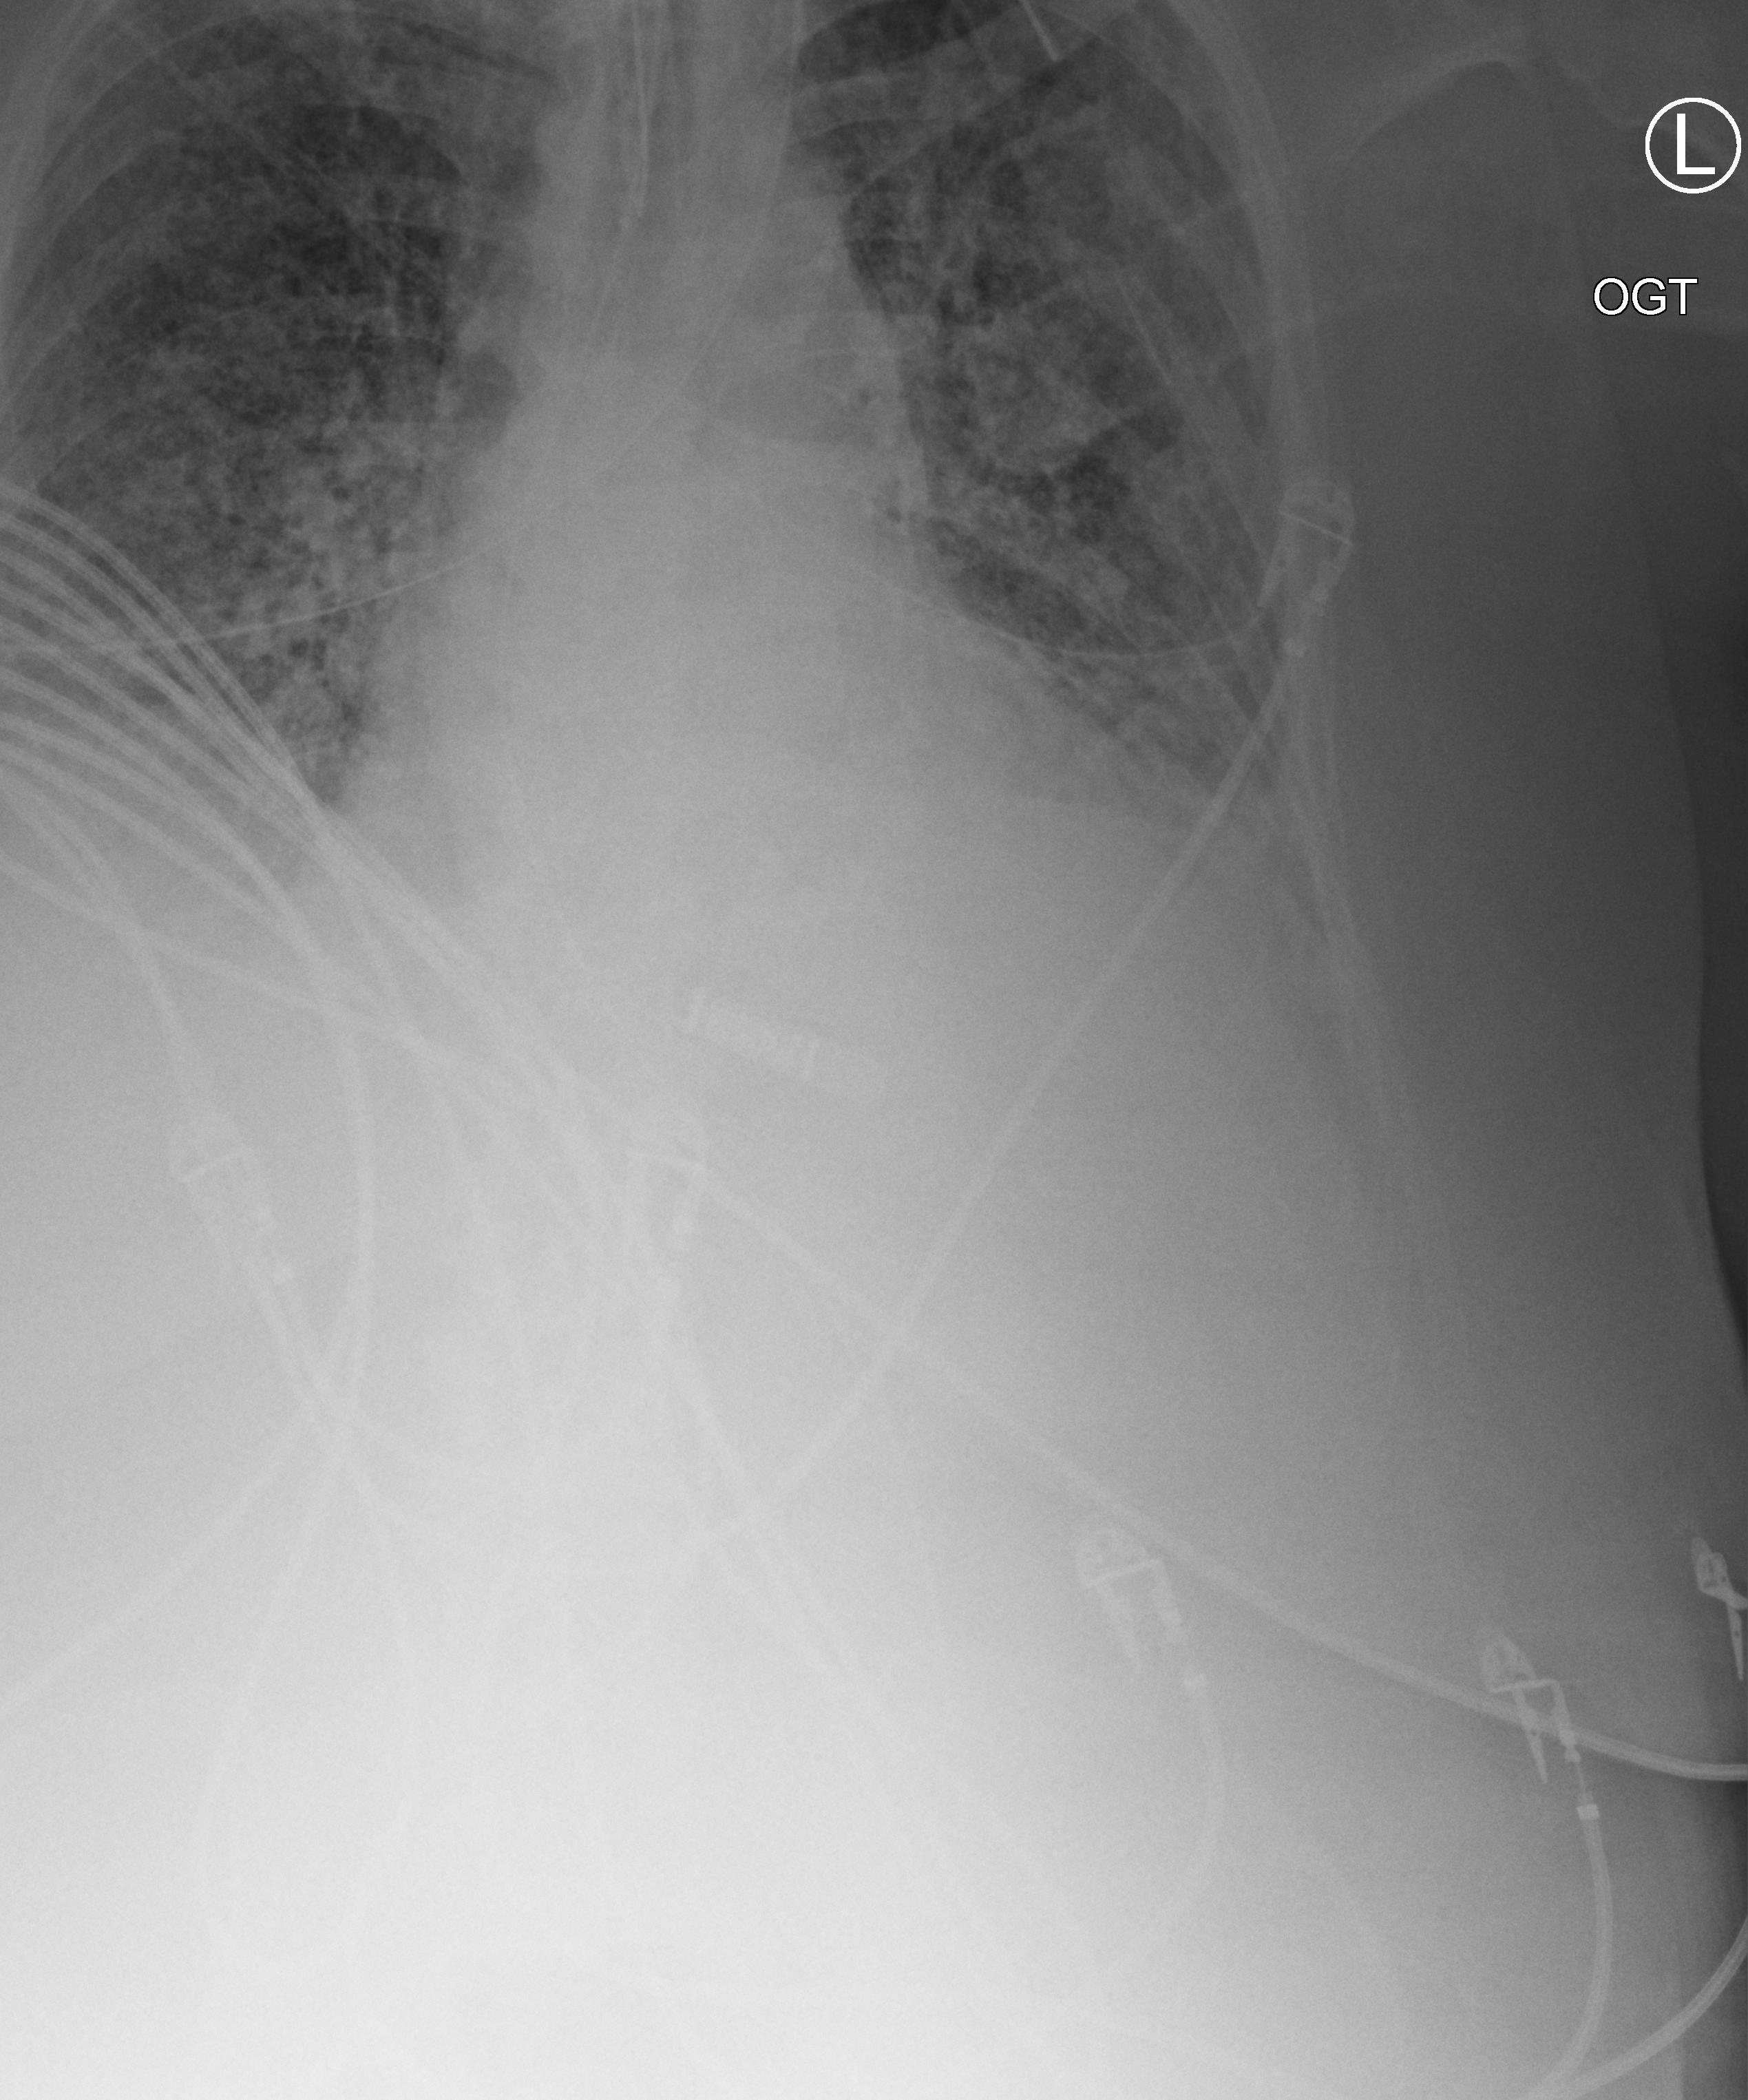
Bedside chest radiograph (computed radiography), anteroposterior (AP) projection. Female patient hospitalised with COVID-19, age 60–74 years.
Hospital-stay facts (about this admission, not read from this image; timing relative to this image not recorded):
- length of hospital stay: 28 days